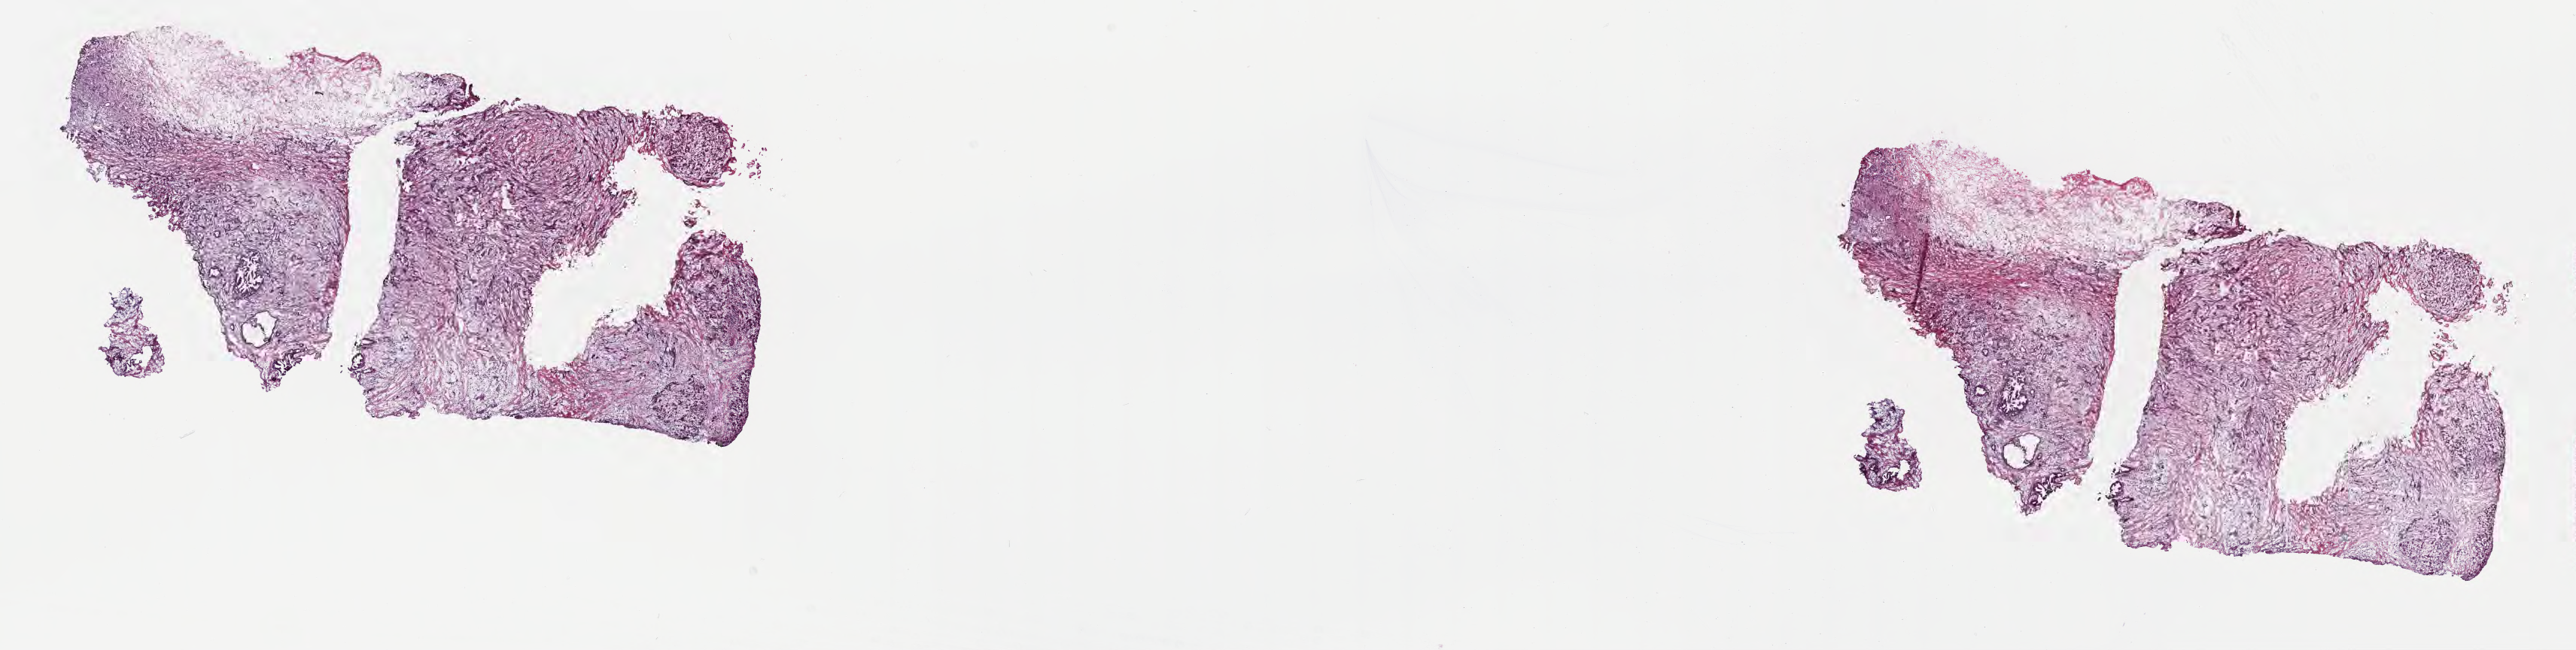
Digitized haematoxylin and eosin-stained section, low-resolution overview of the scanned area, about 27.7 x 7.0 mm. Frozen section (tissue freezing medium). Primary tumor. Anatomic site: head of pancreas. Female patient; age at initial diagnosis 64 years. Pathologist review of this section (percent, as recorded): tumor cells 18%, tumor nuclei 25%, stromal cells 67%, necrosis 15%, normal cells 0%. Infiltration values recorded for this section: lymphocyte infiltration 25%, monocyte infiltration 1%, neutrophil infiltration 0%.
Diagnosis: Infiltrating duct carcinoma, NOS. Section: bottom of the tissue portion.